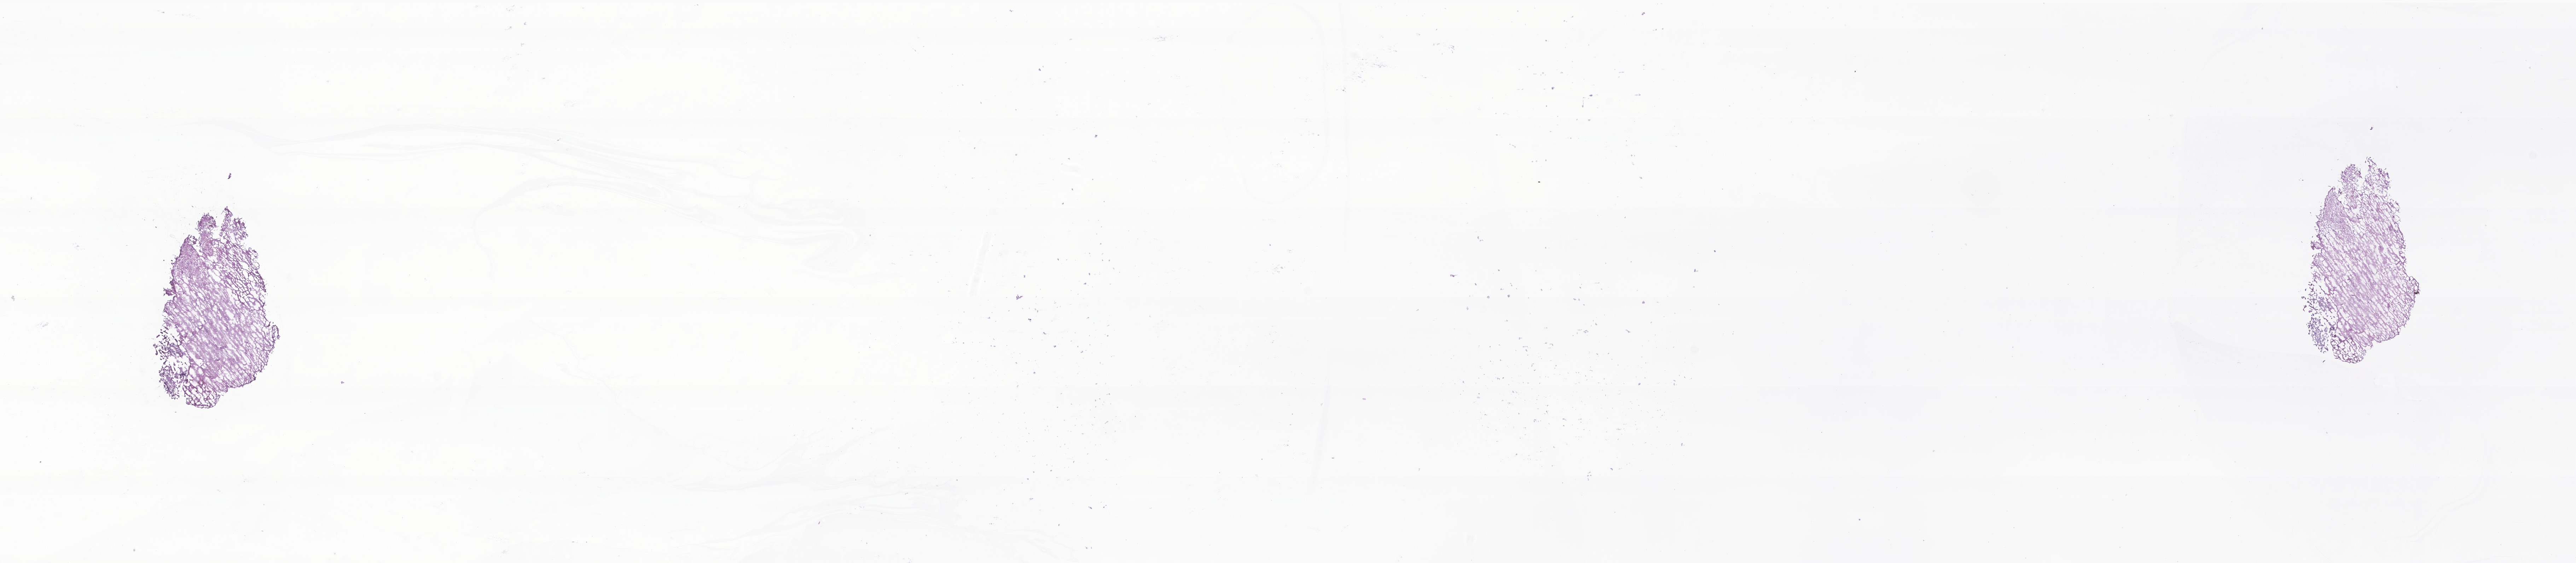
Whole-slide image, H&E stain of tumor tissue from the spinal cord, shown as a low-resolution overview of the whole scanned area (about 30.7 x 6.7 mm), frozen section (OCT-embedded). Patient male; age 201 months (16 years 9 months).
Diagnosis: Glioma, malignant.